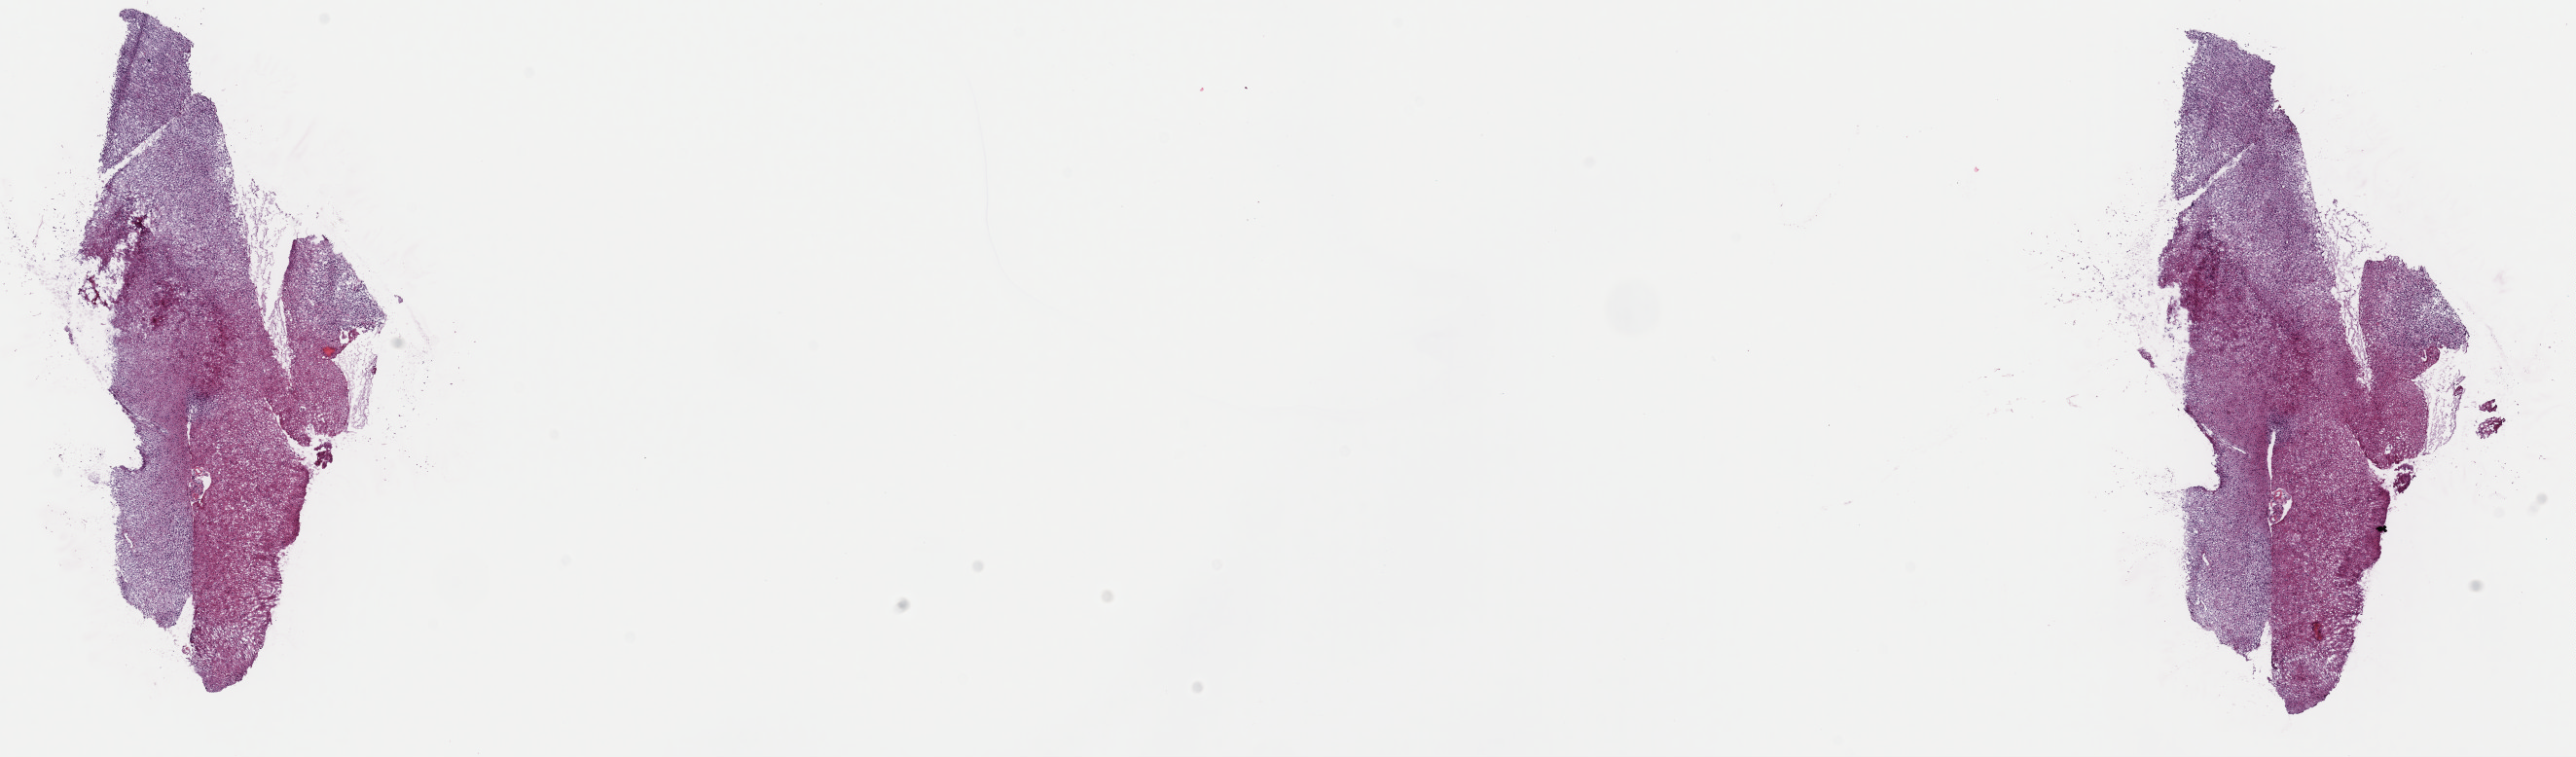
Digitized H&E-stained tissue section (whole slide), a low-resolution overview of the entire scanned area, about 20.9 x 6.1 mm (slide scanned at 40x); frozen section from the top of the tissue portion; primary tumour sample from the brain. Female patient; age at initial diagnosis 38 years. Histologic grade: G2 (moderately differentiated). Composition of this section per pathologist review: tumour cells 50%, tumour nuclei 80%, normal cells 5%, stromal cells 45%, necrosis 0%. Inflammatory infiltration, as recorded: lymphocyte infiltration 0%, monocyte infiltration 0%, neutrophil infiltration 0%.
Laterality: left. Histologic diagnosis: Oligodendroglioma, NOS (cerebrum).